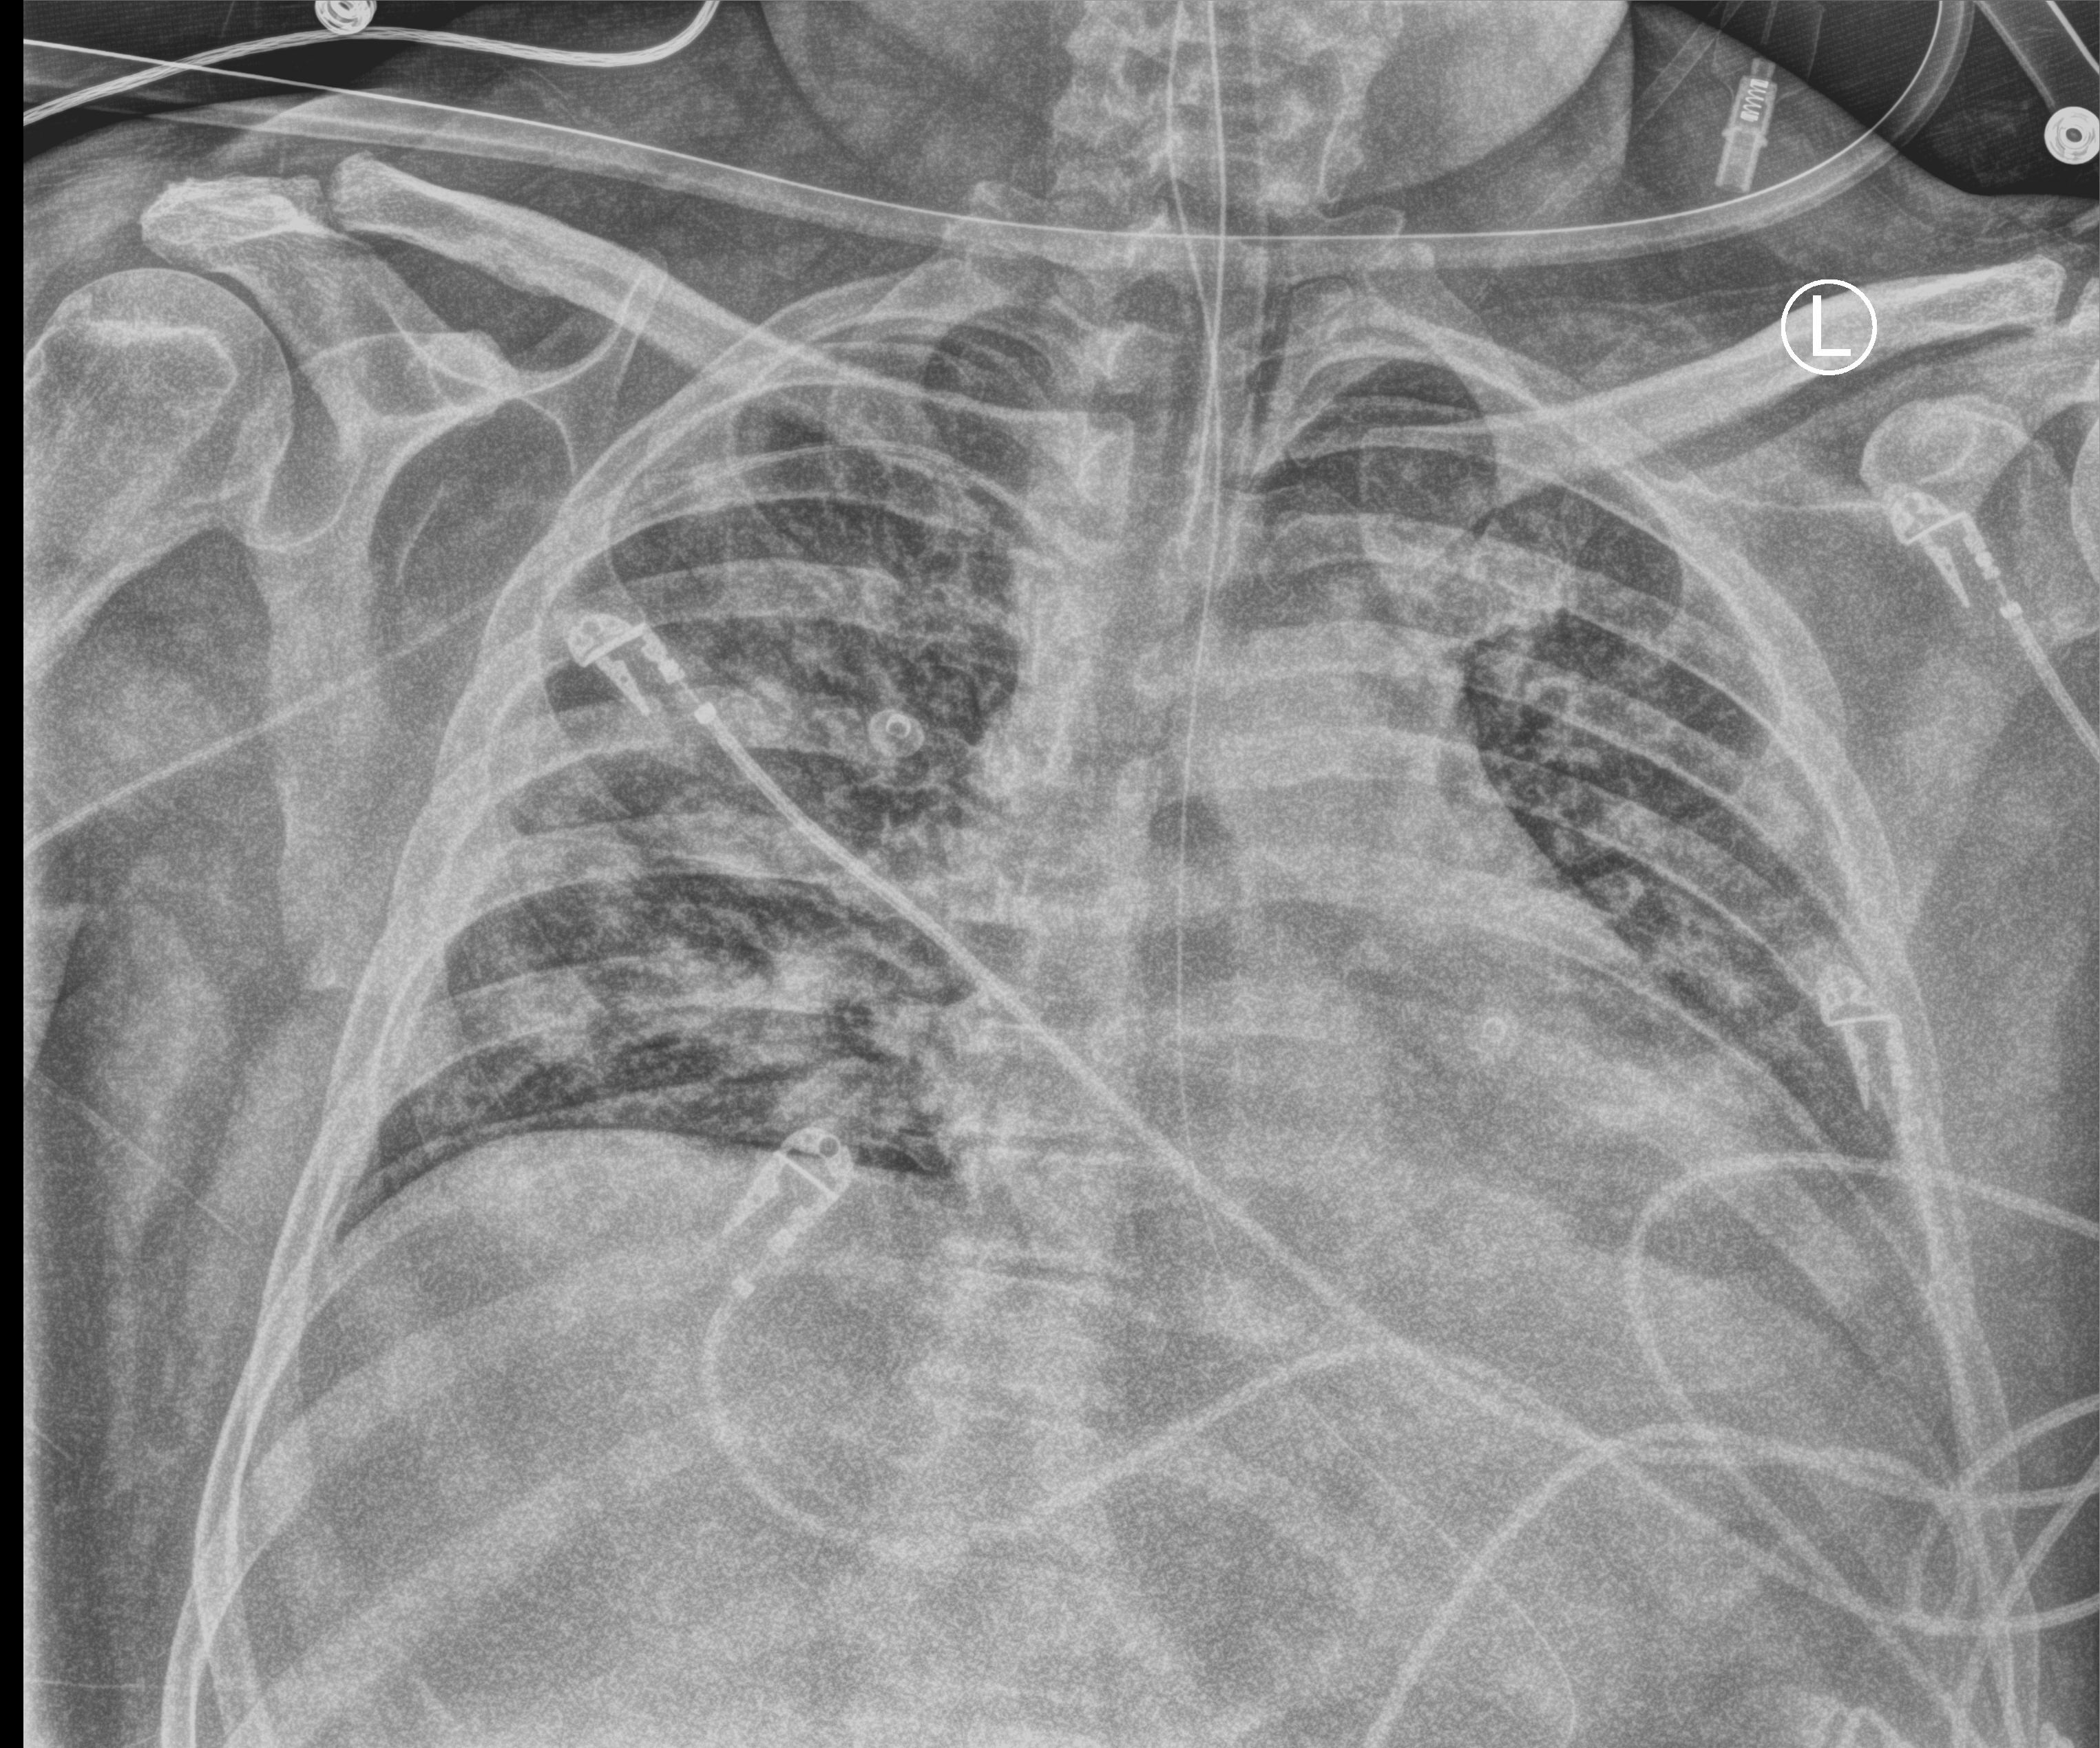
Portable chest radiograph, anteroposterior (AP) projection. Male patient hospitalised with COVID-19, age 18–59 years.
Hospital-stay facts (about this admission, not read from this image; timing relative to this image not recorded):
- length of hospital stay: 30 days
- admitted to intensive care during this hospital stay: yes